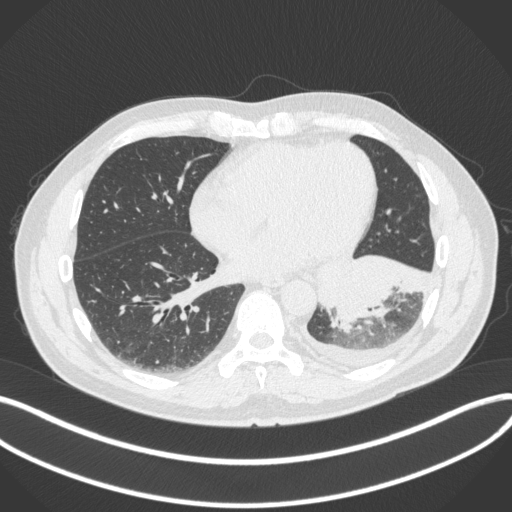
Chest CT, one axial slice; position 131 of 350 along the scan axis; lung window (W 1500 / L -600 HU); 1 mm slice thickness; 512 × 512 image matrix. Male patient, age 58 years. Case-level facts recorded for this patient, not image findings: clinical TNM (as recorded): T3 N1 M1b; histopathological grade: G3.
Annotated regions visible in this slice (rectangle marked by the reading radiologist):
- lung tumour (recorded histology: small cell carcinoma): box from (x=319, y=250) to (x=434, y=331) px